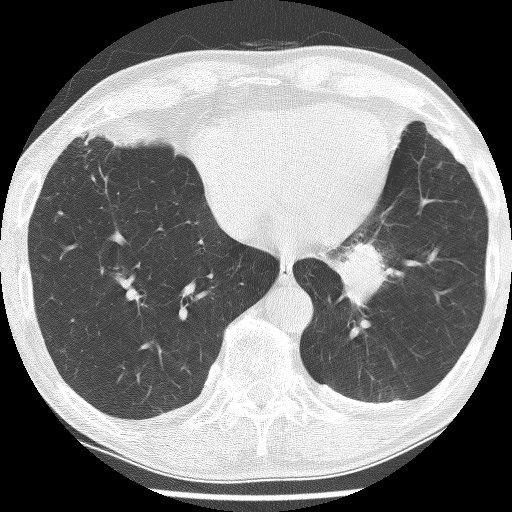
Axial slice from a low-dose chest CT screening exam, baseline screening round, lung window (W 1500 / L -600 HU), 2.5 mm slice thickness, lung (sharp) reconstruction kernel (BONE), slice 174 of 226 in the series. Male participant, aged 74 years at enrolment. Current smoker at enrolment.
- Lesion marked by an expert reader, bounding box (x1, y1, x2, y2) in pixels: (316, 224, 421, 317).
- Screening reader's record for this exam (one nodule recorded; not confirmed to be the boxed lesion): non-calcified nodule or mass ≥4 mm, left lower lobe, 30 × 27 mm, spiculated (stellate) margins, soft tissue attenuation.
- Official screen result: positive, change unspecified: nodule(s) >= 4 mm or enlarging nodule(s), mass(es), or other non-specific abnormalities suspicious for lung cancer.
- Later outcome: lung cancer diagnosed 151 days after this screen — adenocarcinoma, NOS, left lower lobe, stage IIIA (AJCC 6th edition), 49 mm at pathology.